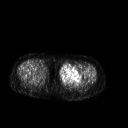
FDG PET of an extremity soft-tissue mass (from a PET/CT study), one axial slice; slice 234 of 267 in the series (ordered by position); 3.27 mm slice thickness; 128 × 128 image matrix, field of view 500 × 500 mm. Female patient, age 42 years. Case-level facts recorded for this patient, not image findings: histological type: pleiomorphic leiomyosarcoma; grade: intermediate; site of the primary tumour: left thigh.
Structures marked on this image (expert contour drawn on MRI and transferred to this co-registered scan by the dataset authors):
- gross tumour volume including surrounding oedema: box from (x=59, y=65) to (x=83, y=84) px
- gross tumour volume (mass): (x=59, y=65)–(x=82, y=83)